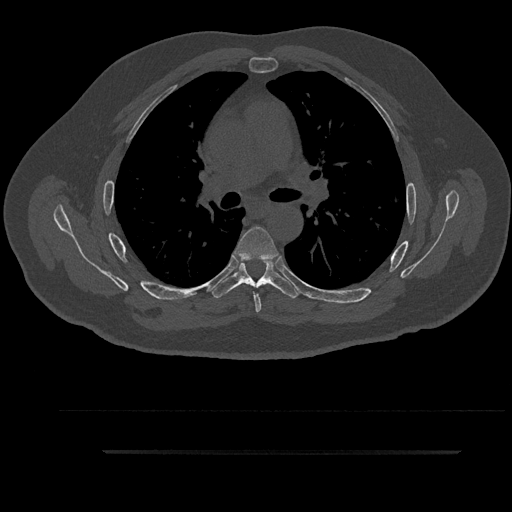
CT including the spine, one axial slice. Slice 602 of 797 in the series (ordered by position). Reconstruction kernel Br40s/3. 120 kVp. Bone window (W 1800 / L 400 HU). 0.5 mm slice thickness. 512 × 512 image matrix, field of view 432 × 432 mm. Patient: male, 63 years. From the clinical record (not read from this slice): primary cancer: renal; vertebrae with lytic lesions (as recorded): T8.
Outlined on this slice (semi-automatic segmentation, software-assisted and operator-edited):
- T5 vertebra: box from (x=233, y=226) to (x=280, y=312) px
- T6 vertebra: (x=211, y=258)–(x=300, y=298)